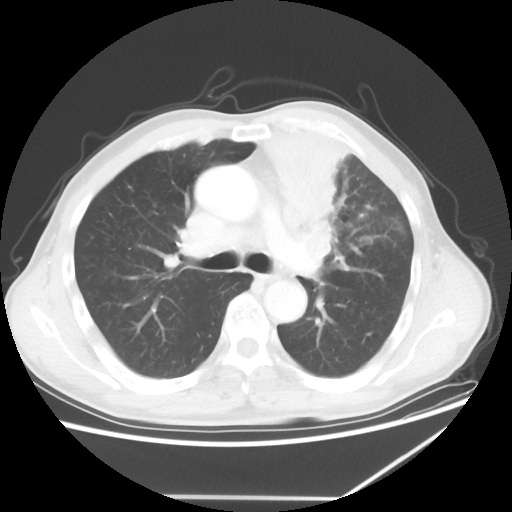
Chest CT, one axial slice; slice 40 of 64 in the series (ordered by position); lung window (W 1500 / L -600 HU); 5 mm slice thickness; 512 × 512 image matrix, field of view 383 × 383 mm. Male patient, age 64 years. Case-level facts recorded for this patient, not image findings: clinical TNM (as recorded): T1c N1 M1; histopathological grade: G2.
Outlined on this slice (rectangle marked by the reading radiologist):
- lung tumour (recorded histology: squamous cell carcinoma): bounding box [x1, y1, x2, y2] px = [269, 128, 378, 253]